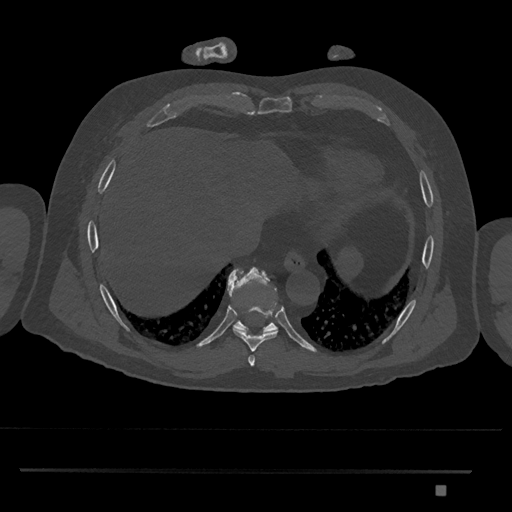
CT including the spine, one axial slice; 120 kVp; bone window (W 1800 / L 400 HU); 0.5 mm slice thickness; 512 × 512 image matrix. Male patient, age 65 years. From the clinical record (not read from this slice): primary cancer: prostate.
Outlined on this slice (semi-automatic segmentation, software-assisted and operator-edited):
- T8 vertebra: bounding box <233,305,278,351> (left, top, right, bottom; pixels)
- T9 vertebra: <228,266,278,333>